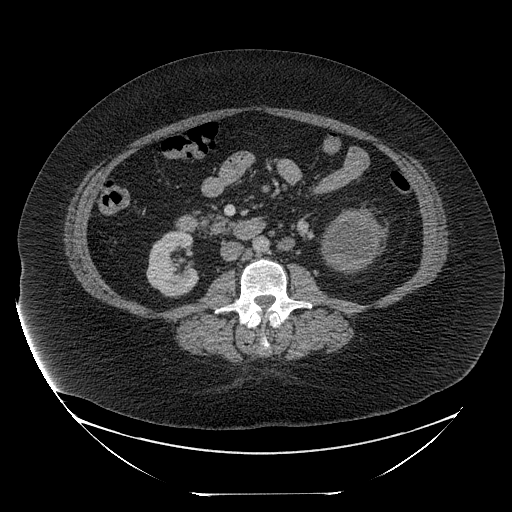
Contrast-enhanced abdominal CT, one axial slice. Soft-tissue window (W 400 / L 40 HU). 2.5 mm slice thickness. 512 × 512 image matrix, field of view 500 × 500 mm. Female patient, age 53 years. Case-level facts recorded for this patient, not image findings: diagnosis: adrenocortical carcinoma; tumour side: left adrenal; tumour size at pathology: 17 cm; Ki-67 index: 20 %; stage (as recorded): 3.
Structures marked on this image (semi-automatically segmented with operator editing):
- mass: box from (x=324, y=210) to (x=380, y=271) px